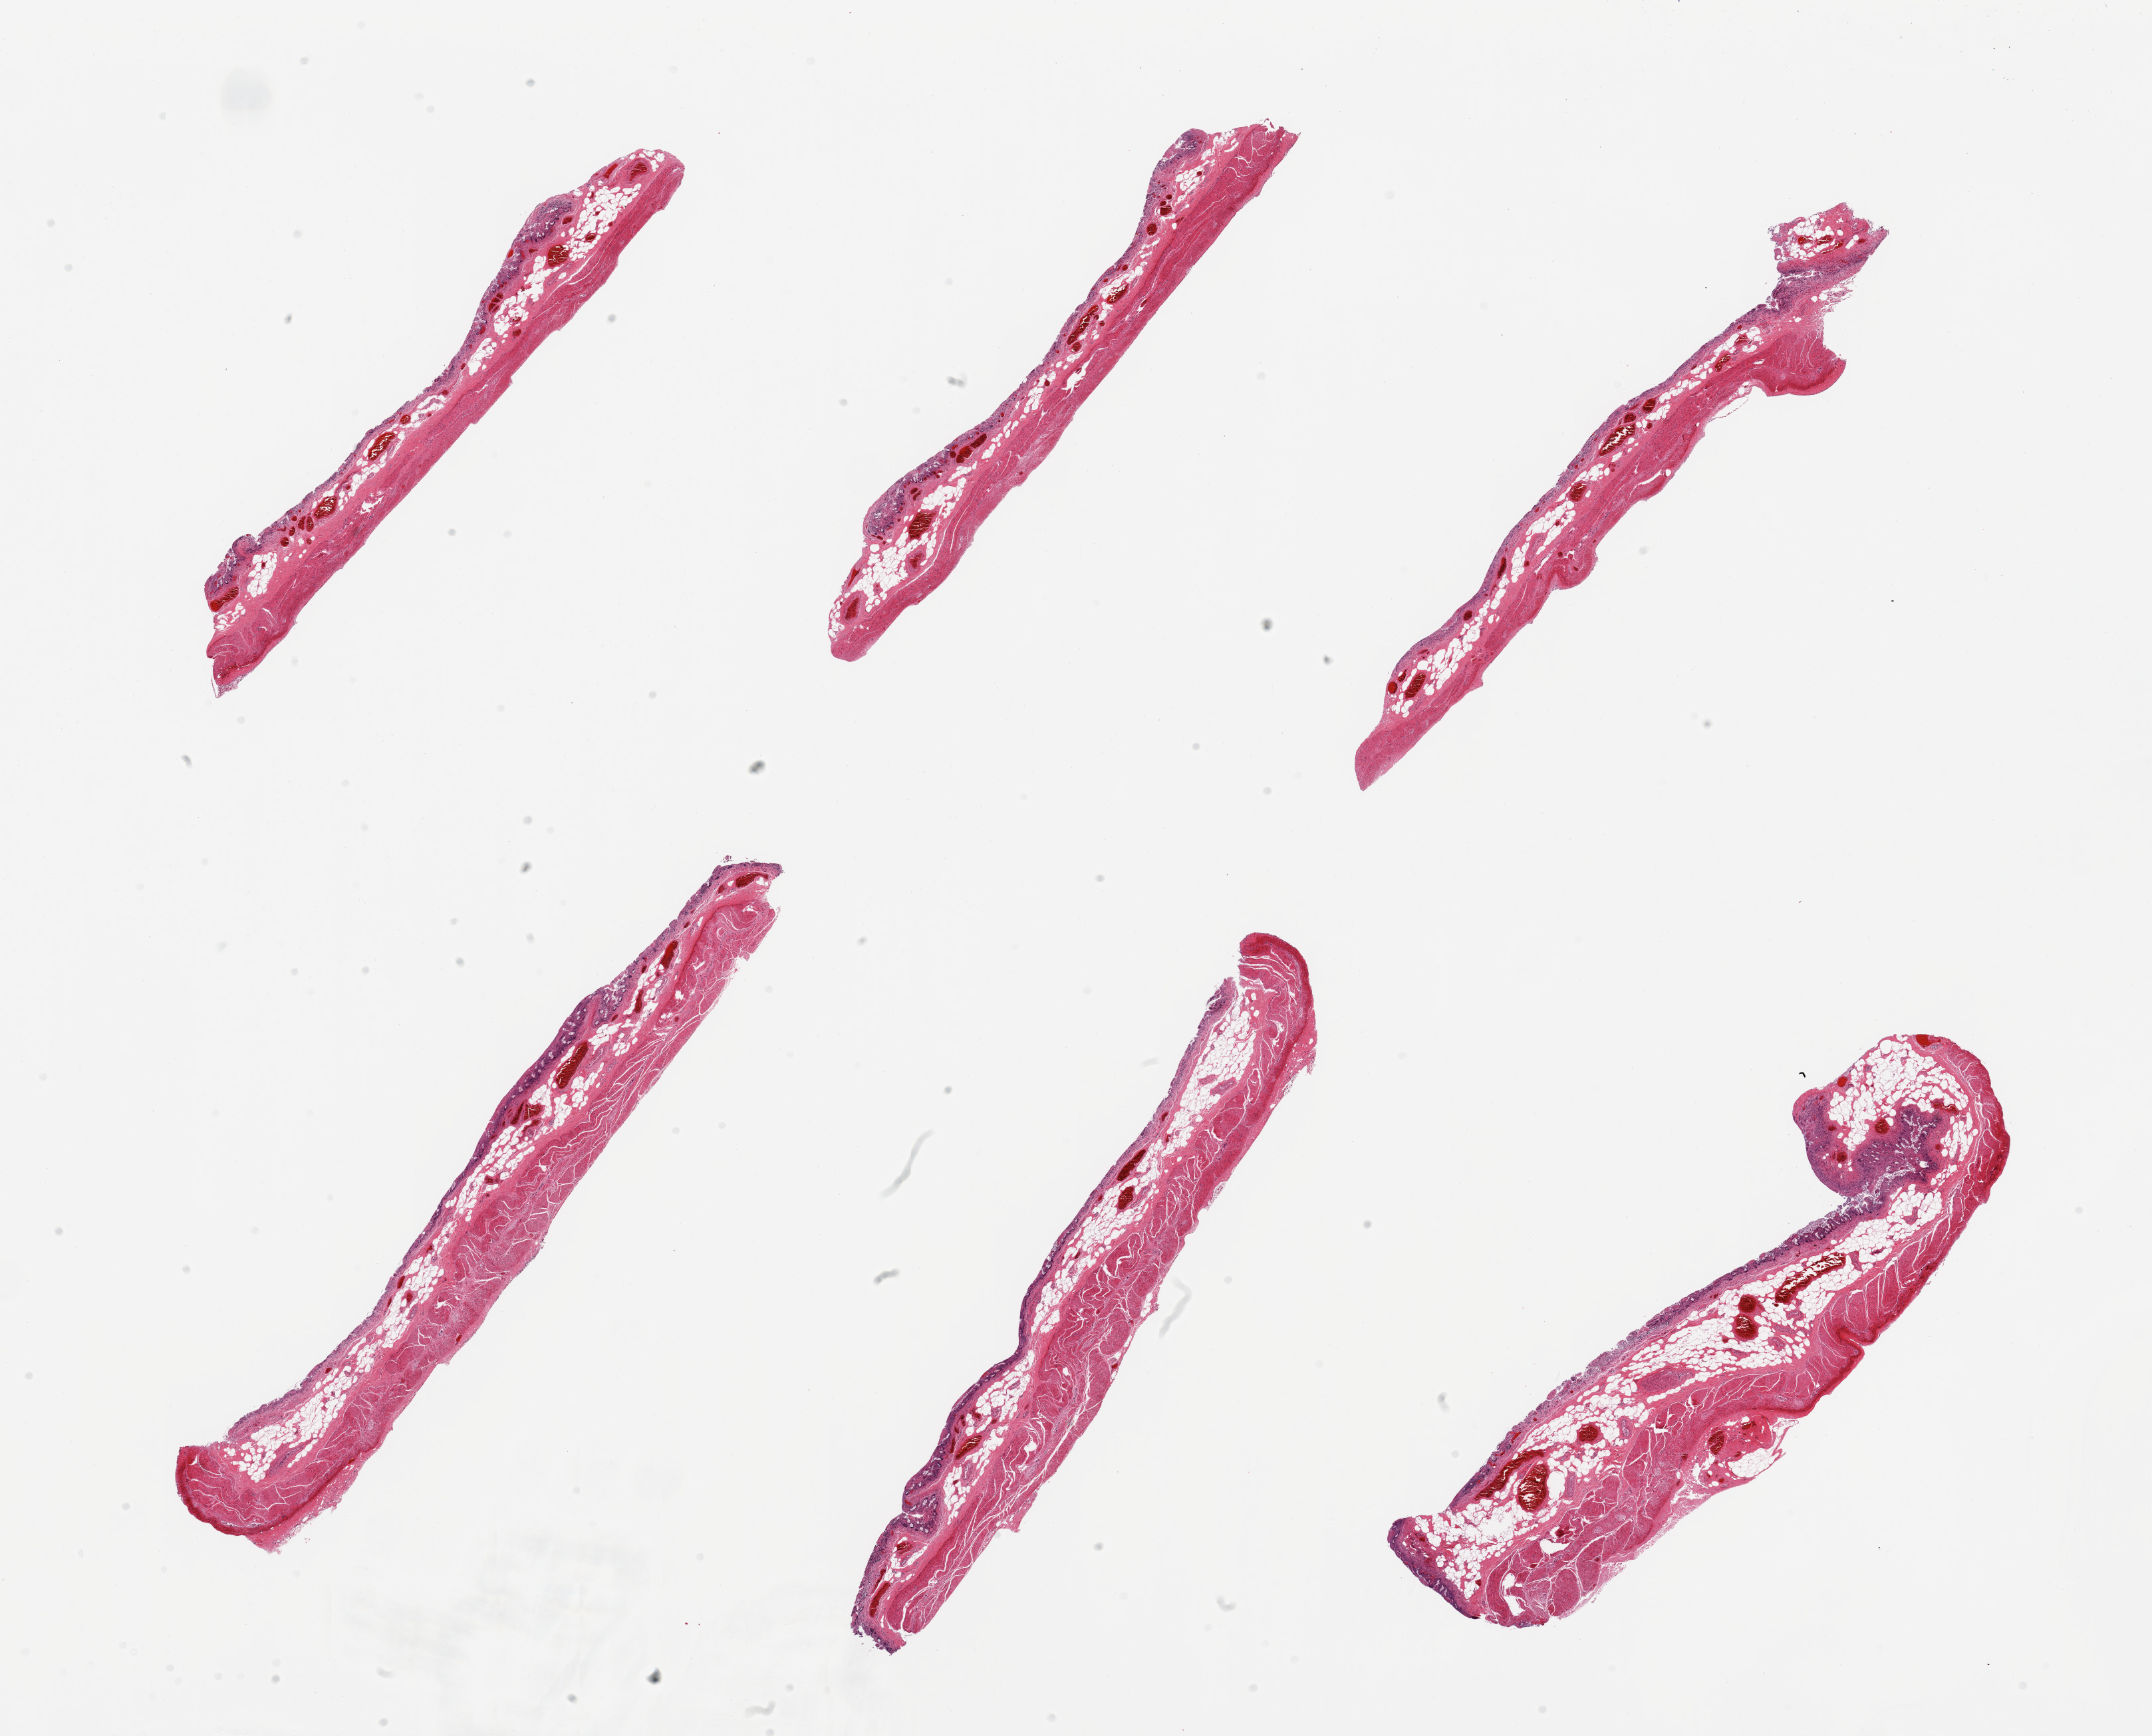
H&E whole-slide image — shown as a low-resolution overview of the whole scanned area (about 25.6 x 20.7 mm); PAXgene-fixed paraffin-embedded (PFPE) section; sampled site (target tissue): ileum; tissue donor sample. Donor: female.
Review note (as recorded): 6 pieces, target mucosa; glandular elements autolyzed, insufficient target lymphoid aggregate to warrant analysis.